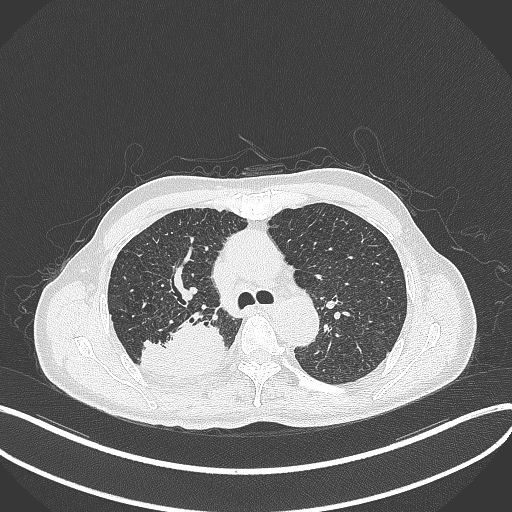
Chest CT, one axial slice. Slice 309 of 428 in the series (ordered by position). Lung window (W 1500 / L -600 HU). 512 × 512 image matrix, field of view 400 × 400 mm. Male patient, age 79 years. From the clinical record (not read from this slice): clinical TNM (as recorded): T3 N0 M0.
Outlined on this slice (bounding box drawn by a radiologist):
- lung tumour (recorded histology: adenocarcinoma): bounding box <139,307,229,382> (left, top, right, bottom; pixels)